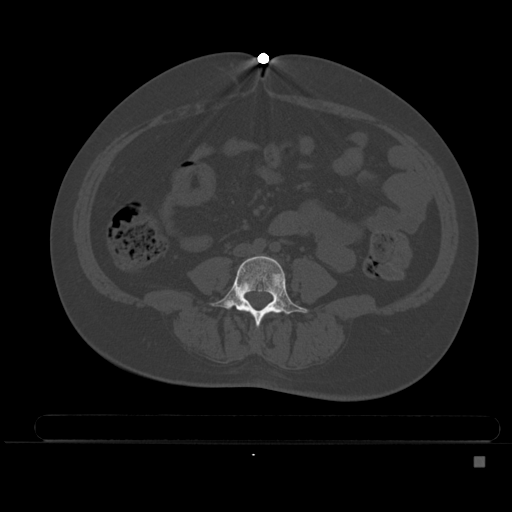
CT including the spine, one axial slice; slice 131 of 495 in the series (ordered by position); bone window (W 1800 / L 400 HU); 1.5 mm slice thickness; 512 × 512 image matrix. Patient: female, 33 years. From the clinical record (not read from this slice): primary cancer: breast.
Structures marked on this image (semi-automatic segmentation, software-assisted and operator-edited):
- L4 vertebra: bounding box [x1, y1, x2, y2] px = [209, 255, 309, 326]